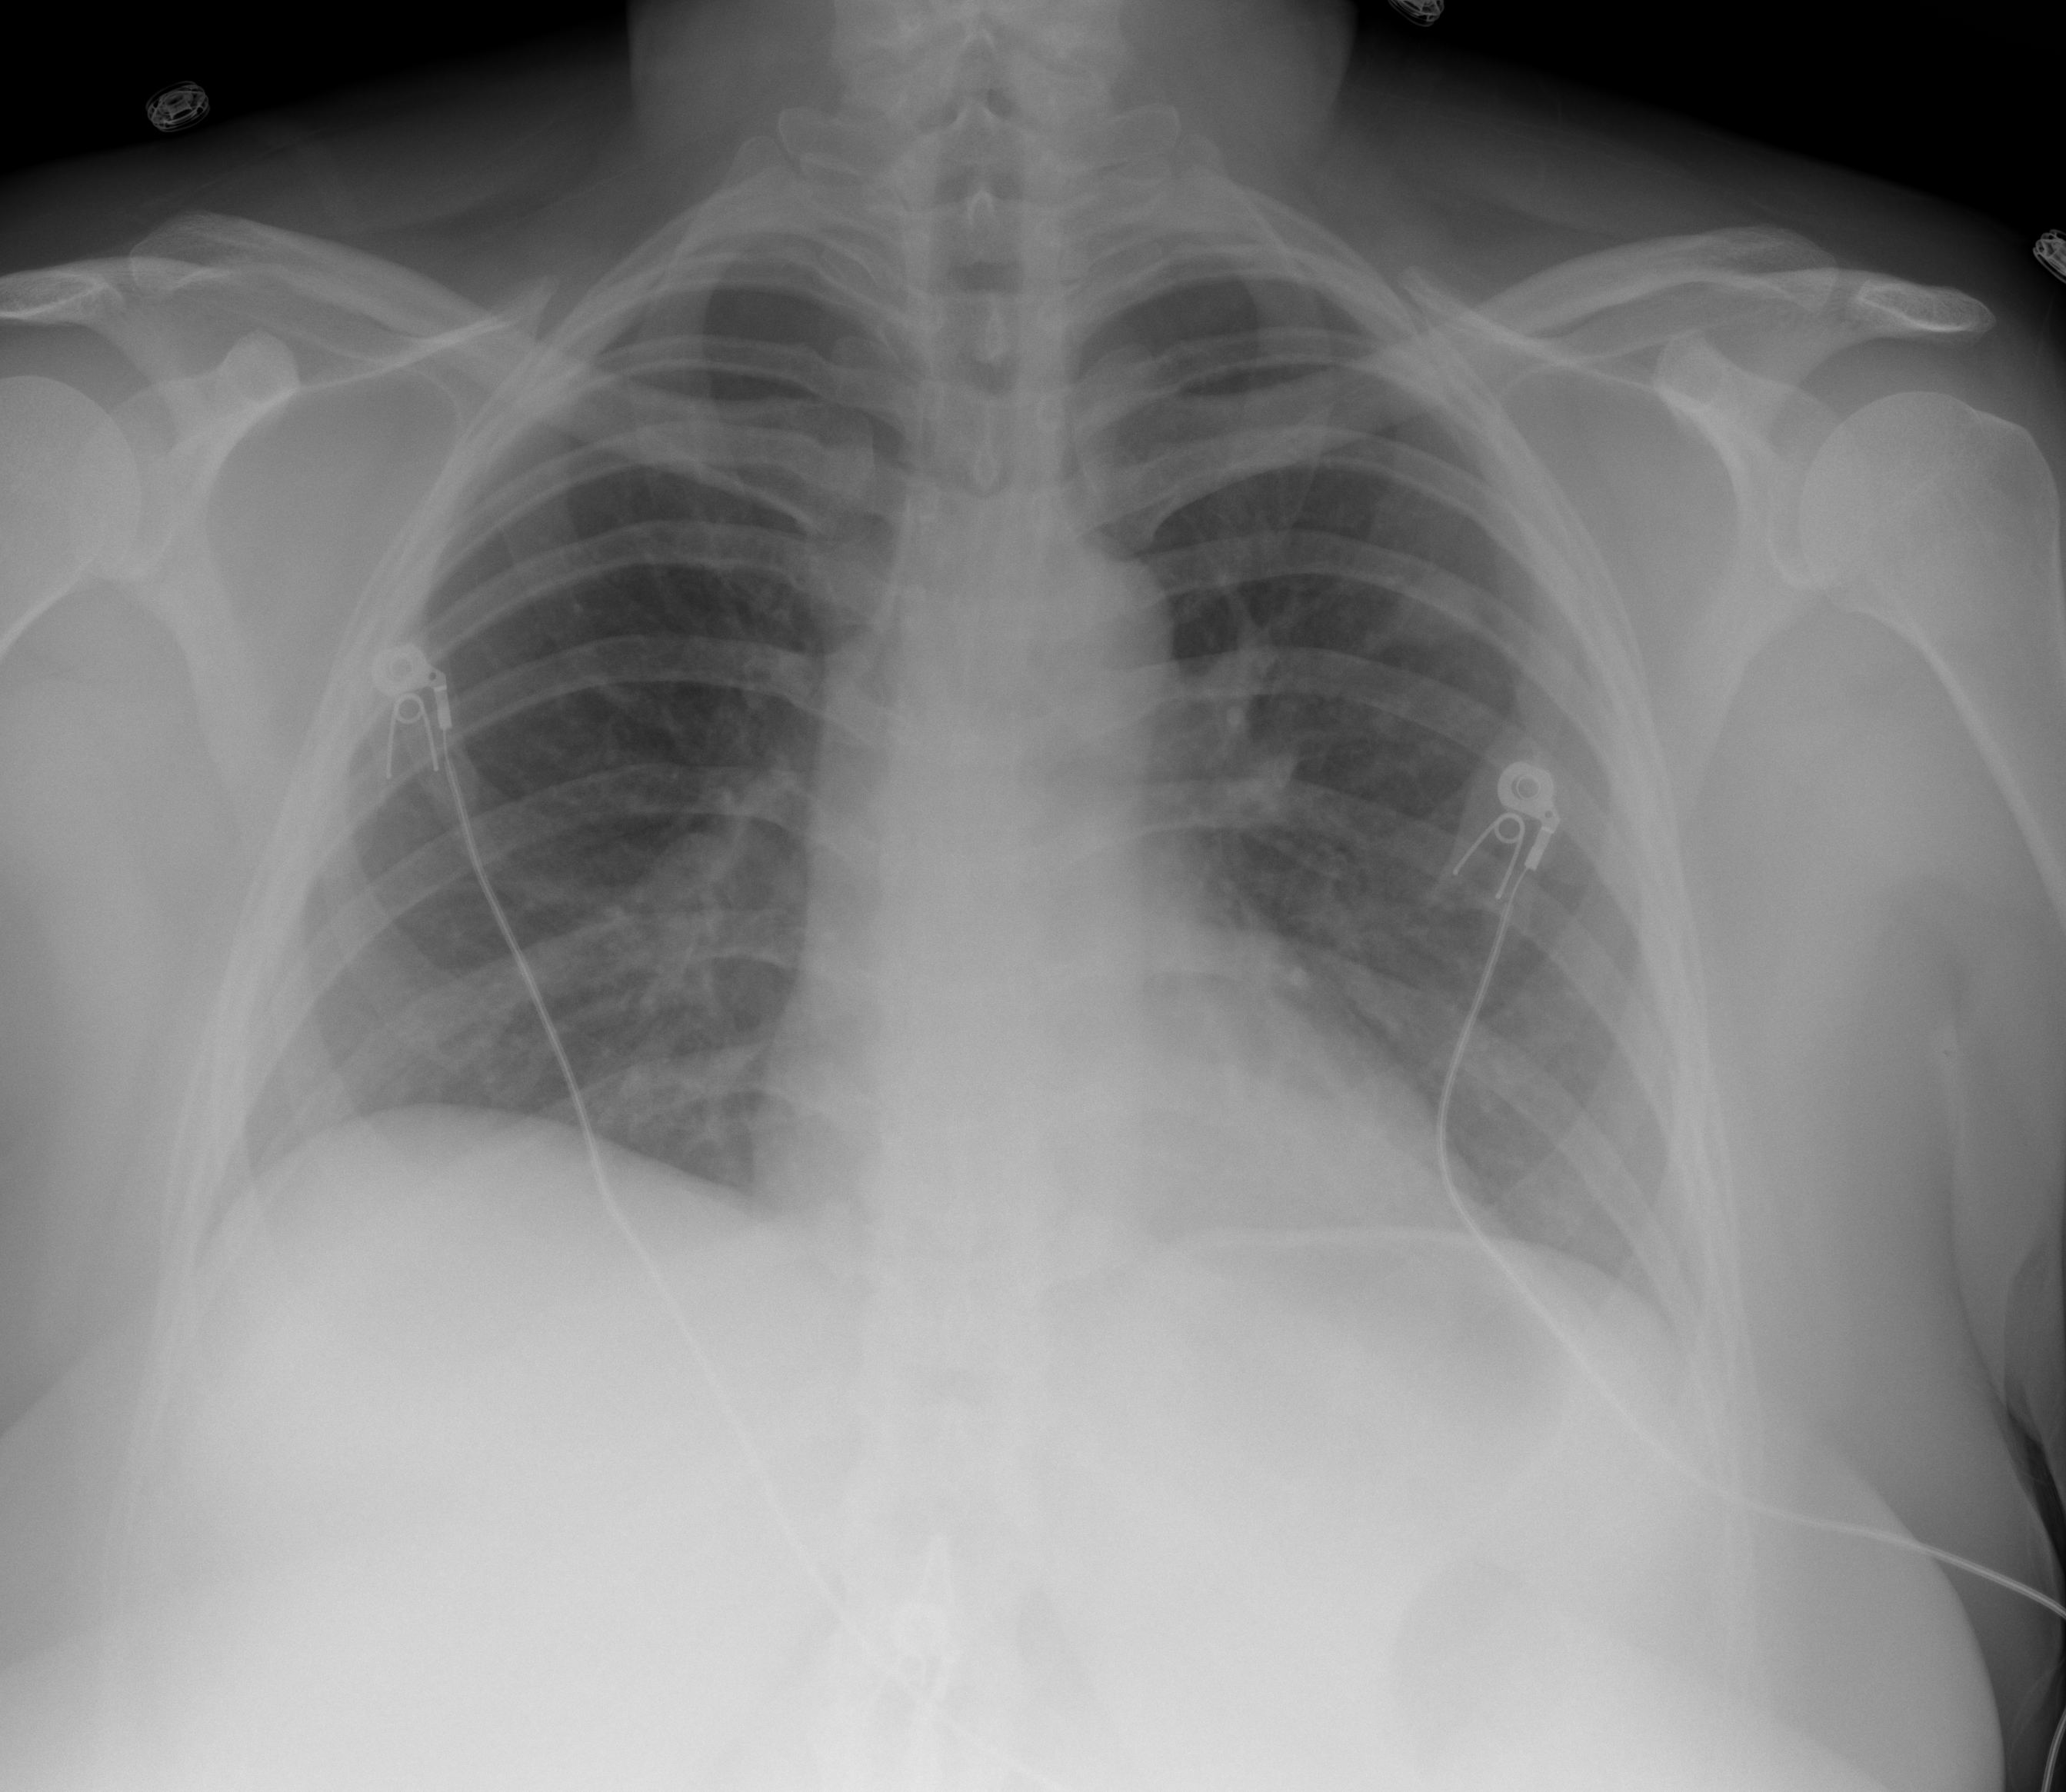
Portable chest radiograph, AP projection. Female patient, age 40 years; imaged 0 days after the COVID-19 diagnosis.
Radiologist key findings (as recorded): Indeterminate 2 cm left upper nodule, felt to represent a calcified granuloma.